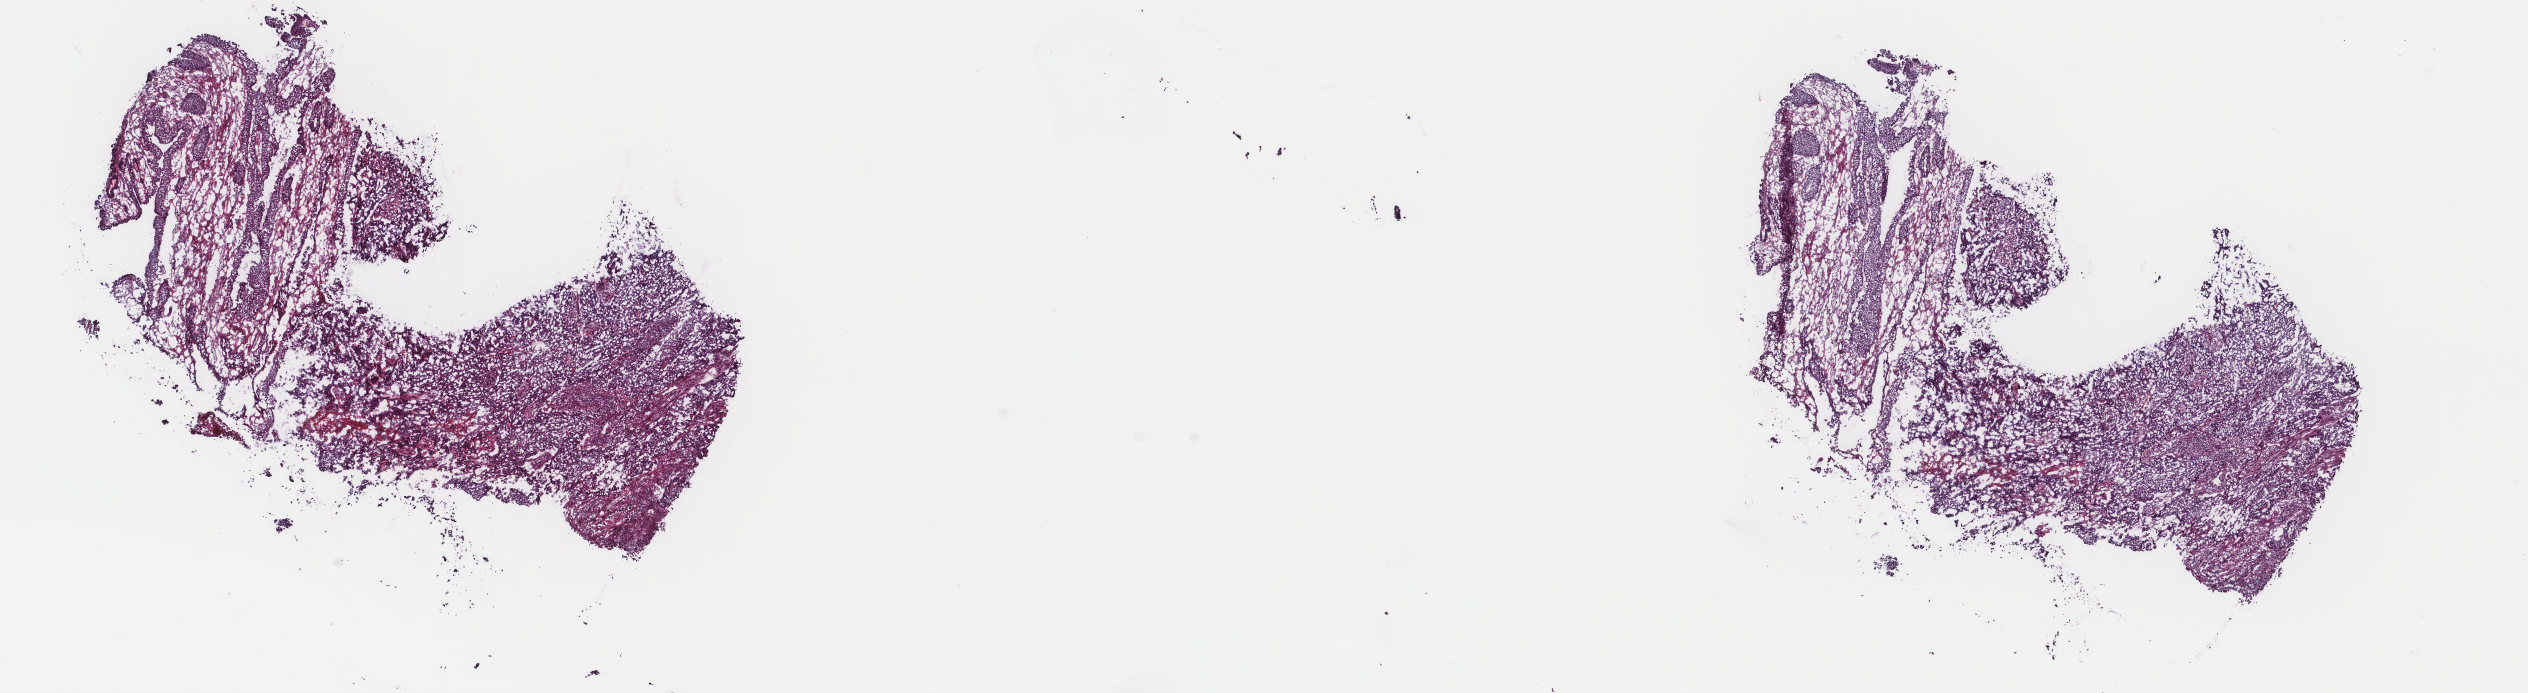
Whole-slide histology image, H&E-stained, shown as a low-resolution overview of the whole scanned area (about 20.1 x 5.5 mm, acquisition: 40x scan), frozen section from the top of the tissue portion, primary tumour sample from the bladder. Male, age 60 years at initial diagnosis. Histologic grade: high grade. Slide review estimates, as recorded: tumour cells 75%, tumour nuclei 75%, normal cells 0%, stromal cells 25%, necrosis 0%. Inflammatory infiltration, as recorded: lymphocyte infiltration 5%, monocyte infiltration 2%, neutrophil infiltration 2%.
• TNM: T2b N0 MX
• lymph nodes positive (case pathology): 0 of 85 examined
• pathologic diagnosis: Transitional cell carcinoma (posterior wall of bladder)
• AJCC pathologic stage: II (6th edition)